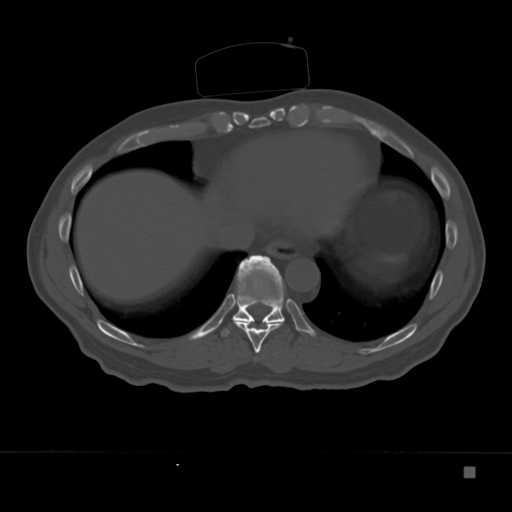
CT including the spine, one axial slice. Reconstruction kernel Br40s. Bone window (W 1800 / L 400 HU). 1.5 mm slice thickness. 512 × 512 image matrix. Patient: male, 72 years. From the clinical record (not read from this slice): primary cancer: skeletal.
Annotated regions visible in this slice (semi-automatic segmentation, software-assisted and operator-edited):
- T10 vertebra: bounding box [x1, y1, x2, y2] px = [221, 255, 285, 336]
- T9 vertebra: [234, 320, 284, 354]